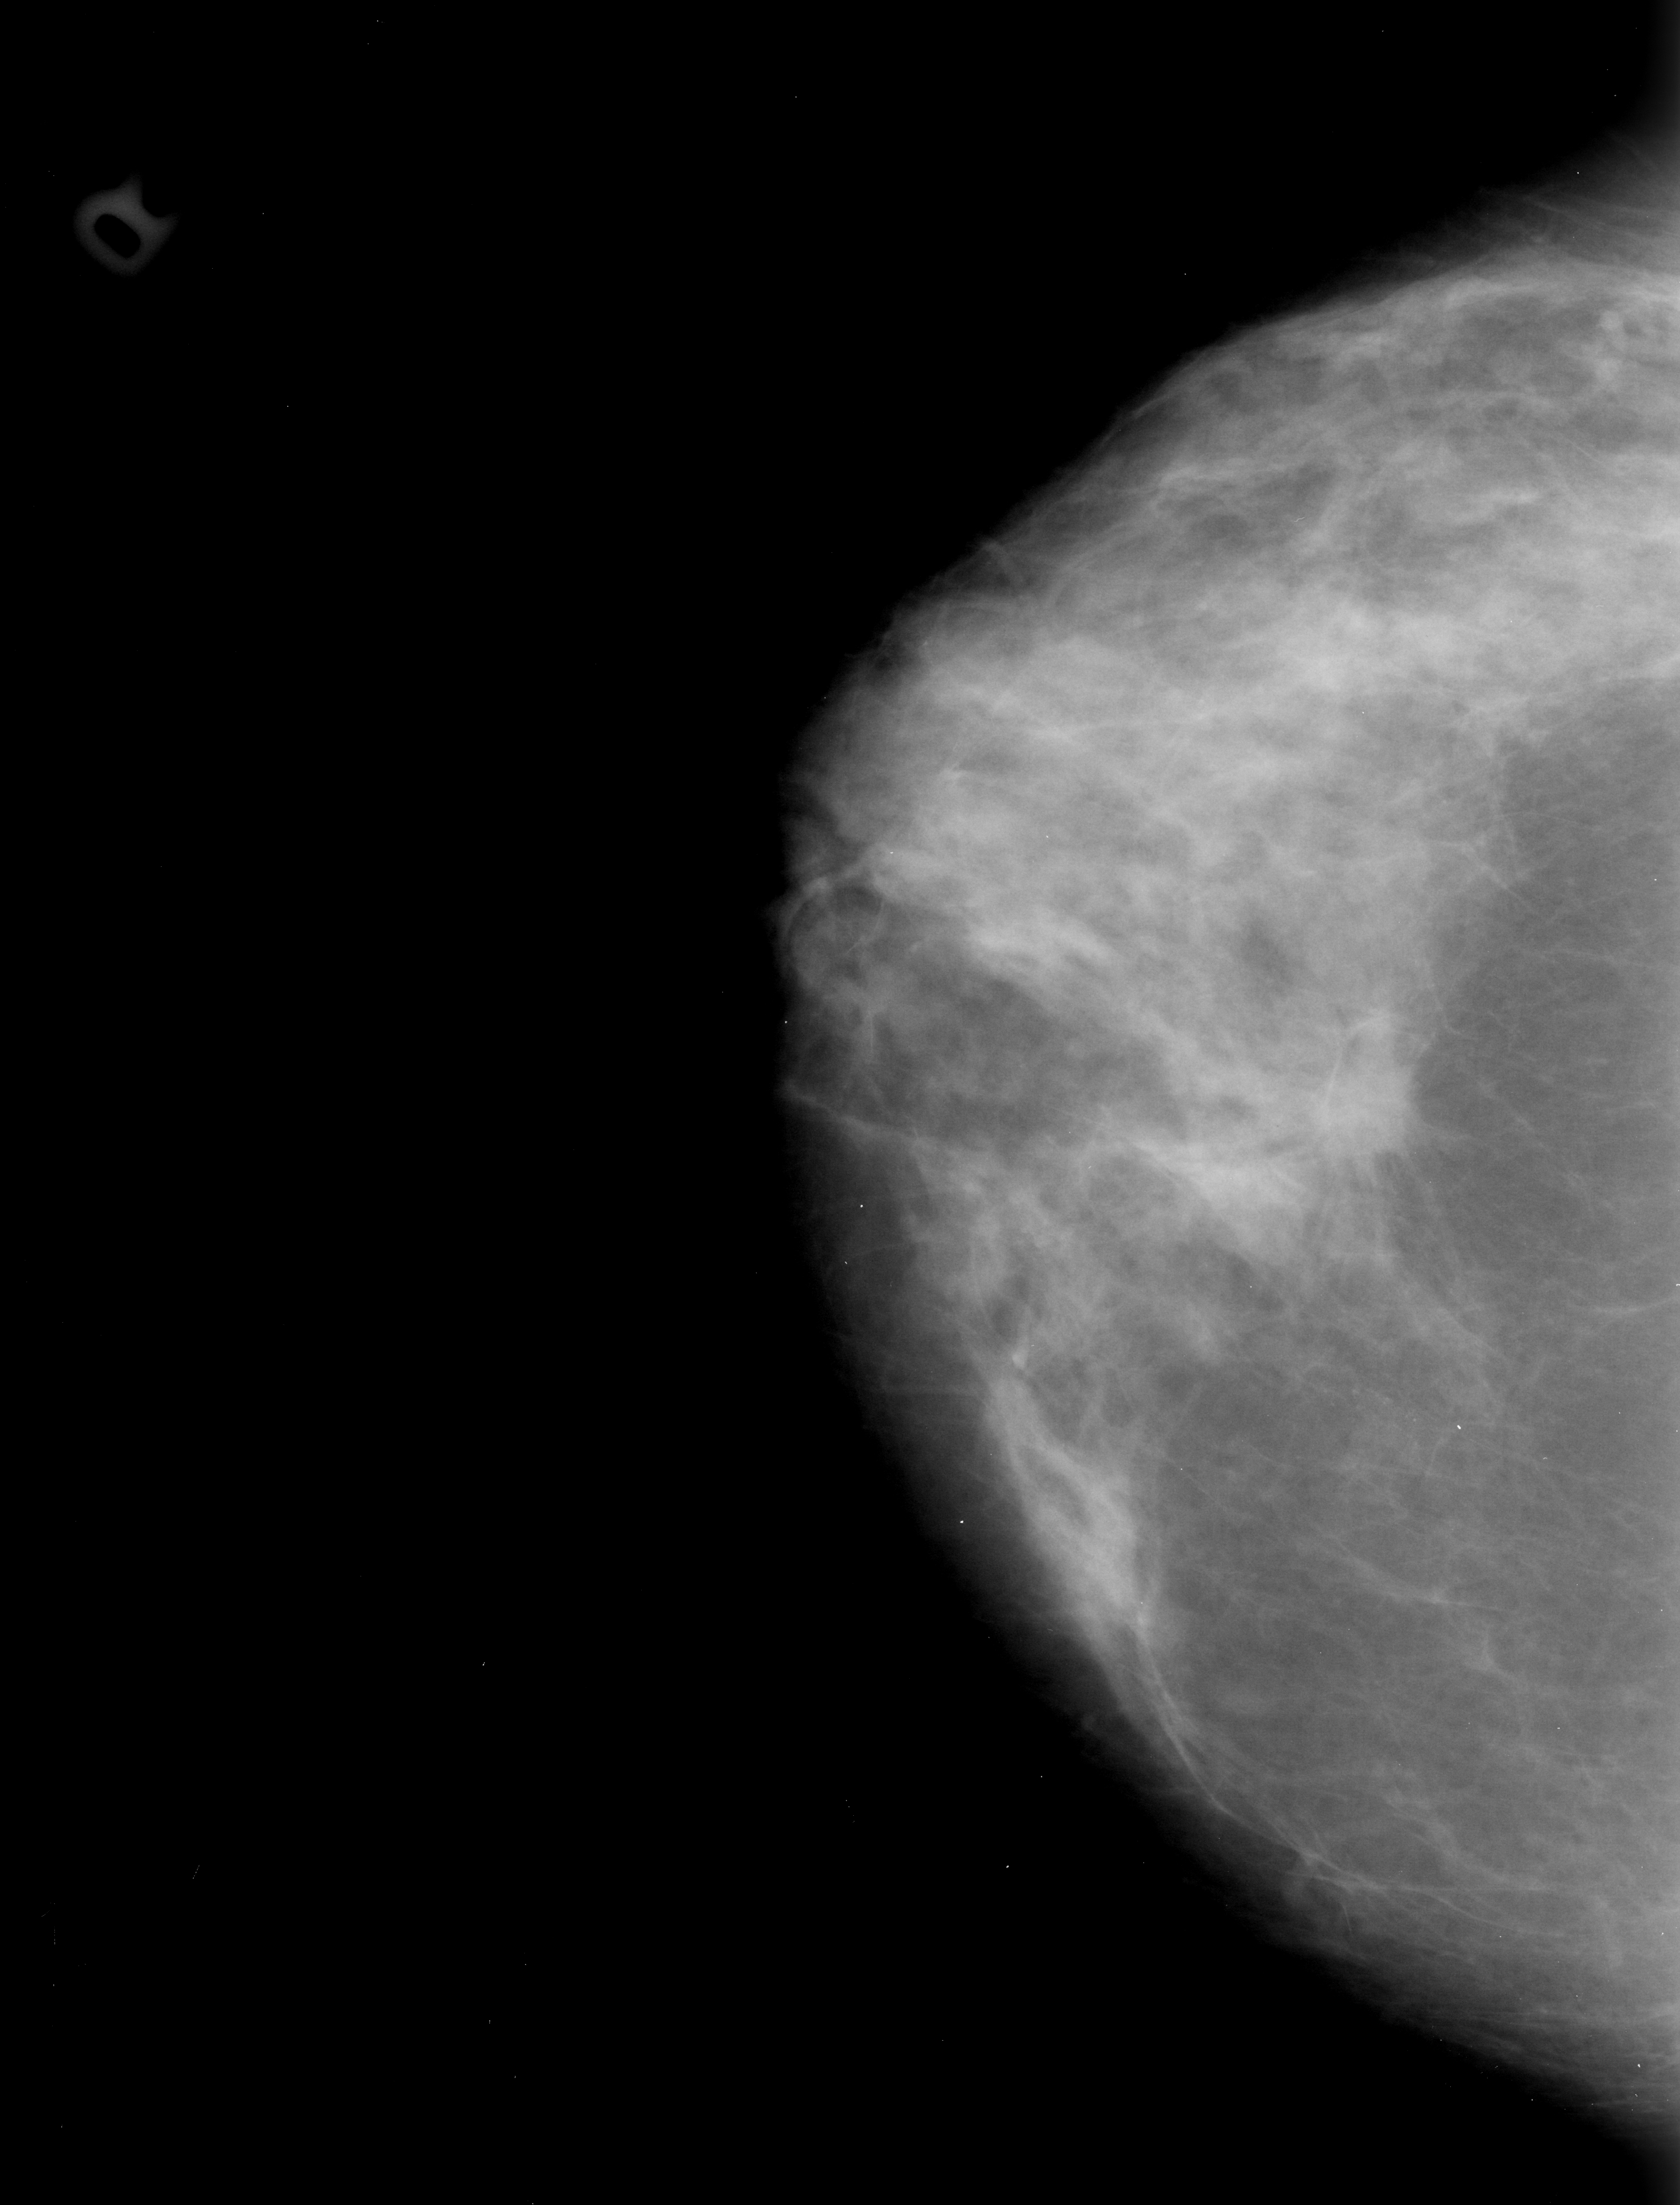
Scanned film-screen mammogram. Right breast. Craniocaudal (CC) view. 1680 × 2205 image matrix.
Marked abnormalities (boxes around the expert regions of interest):
- mass, shape irregular / architectural distortion, margins spiculated; BI-RADS assessment category 4; subtlety rating 3 on a 1 (subtle) to 5 (obvious) scale; pathology result (as recorded, not read from the image): malignant: bounding box [x1, y1, x2, y2] px = [1312, 1051, 1452, 1189]